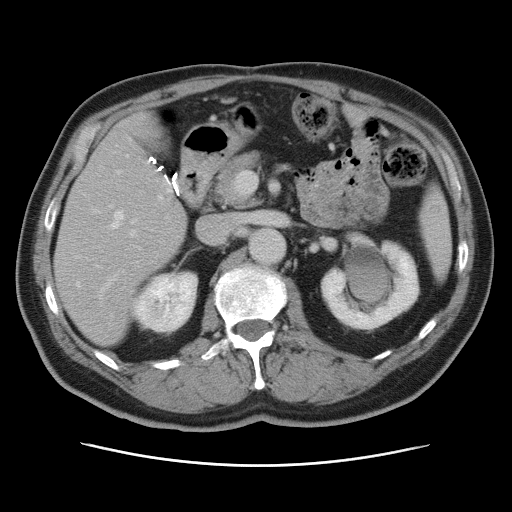
Contrast-enhanced abdominal CT, one axial slice; slice 39 of 80 in the series (ordered by position); intravenous contrast given; soft-tissue window (W 400 / L 40 HU); 5 mm slice thickness; 512 × 512 image matrix, field of view 370 × 370 mm. Male patient, age 69 years. From the clinical record (not read from this slice): diagnosis: colorectal cancer liver metastases, imaged before liver resection; multiple liver metastases: no; largest metastasis: 5 cm; chemotherapy before resection: no.
Outlined on this slice (expert manual segmentation):
- hepatic veins: bounding box [x1, y1, x2, y2] px = [76, 209, 136, 316]
- liver: [55, 114, 187, 344]
- planned liver remnant (the part of the liver to remain after resection): [55, 191, 187, 344]
- portal vein (with intrahepatic branches): [101, 171, 141, 293]